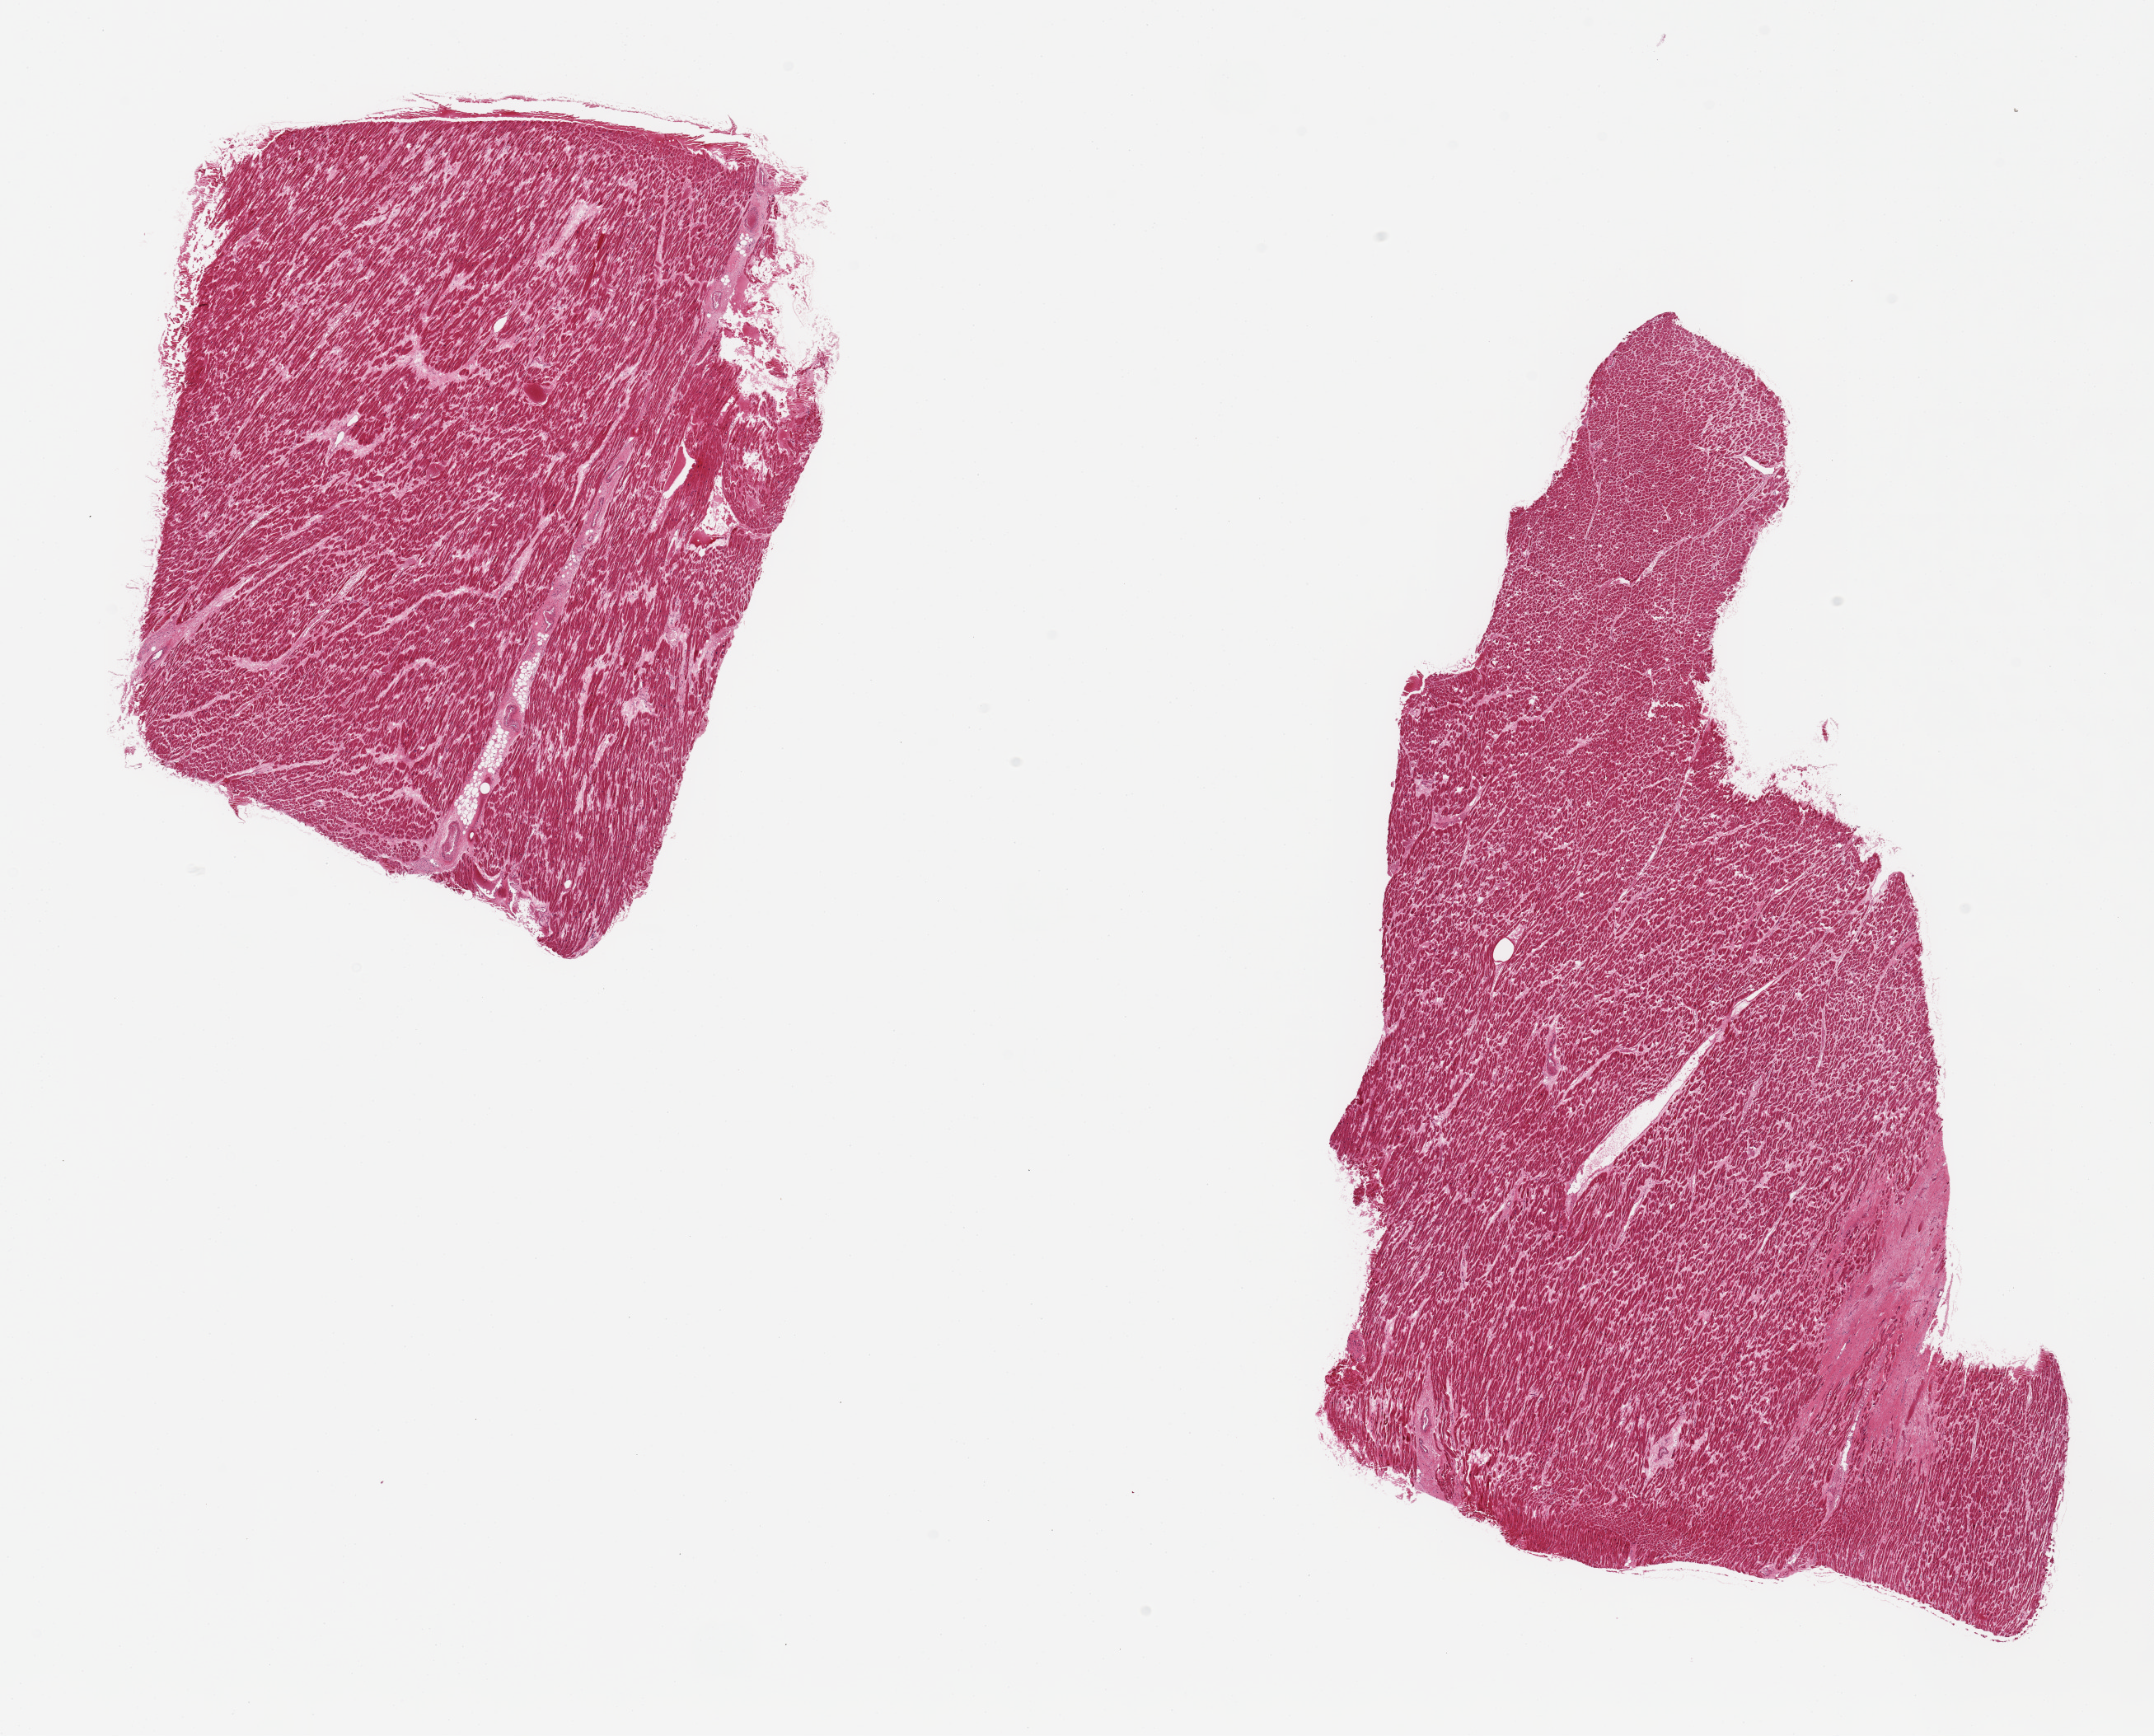
Hematoxylin and eosin (H&E) whole-slide image — a low-resolution overview of the entire scanned area, about 20.7 x 16.7 mm (slide scanned at 20x), PAXgene-fixed, paraffin-embedded tissue, sampled site (target tissue): heart, tissue donor sample. Donor: male.
• pathologist's review note for this sample: 2 pieces, moderate interstitial fibrosis with ~3mm remote infarct